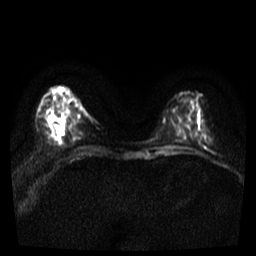
Breast MRI, one axial slice; position 10 of 36 along the scan axis; diffusion-weighted series; image 2 of 4 stored at this slice position (different b-values; order by instance number); 3 T; 5 mm slice thickness; 256 × 256 image matrix. Female patient.
Annotated regions visible in this slice (expert manual segmentation):
- tumour on diffusion-weighted imaging: bounding box <57,126,61,135> (left, top, right, bottom; pixels)